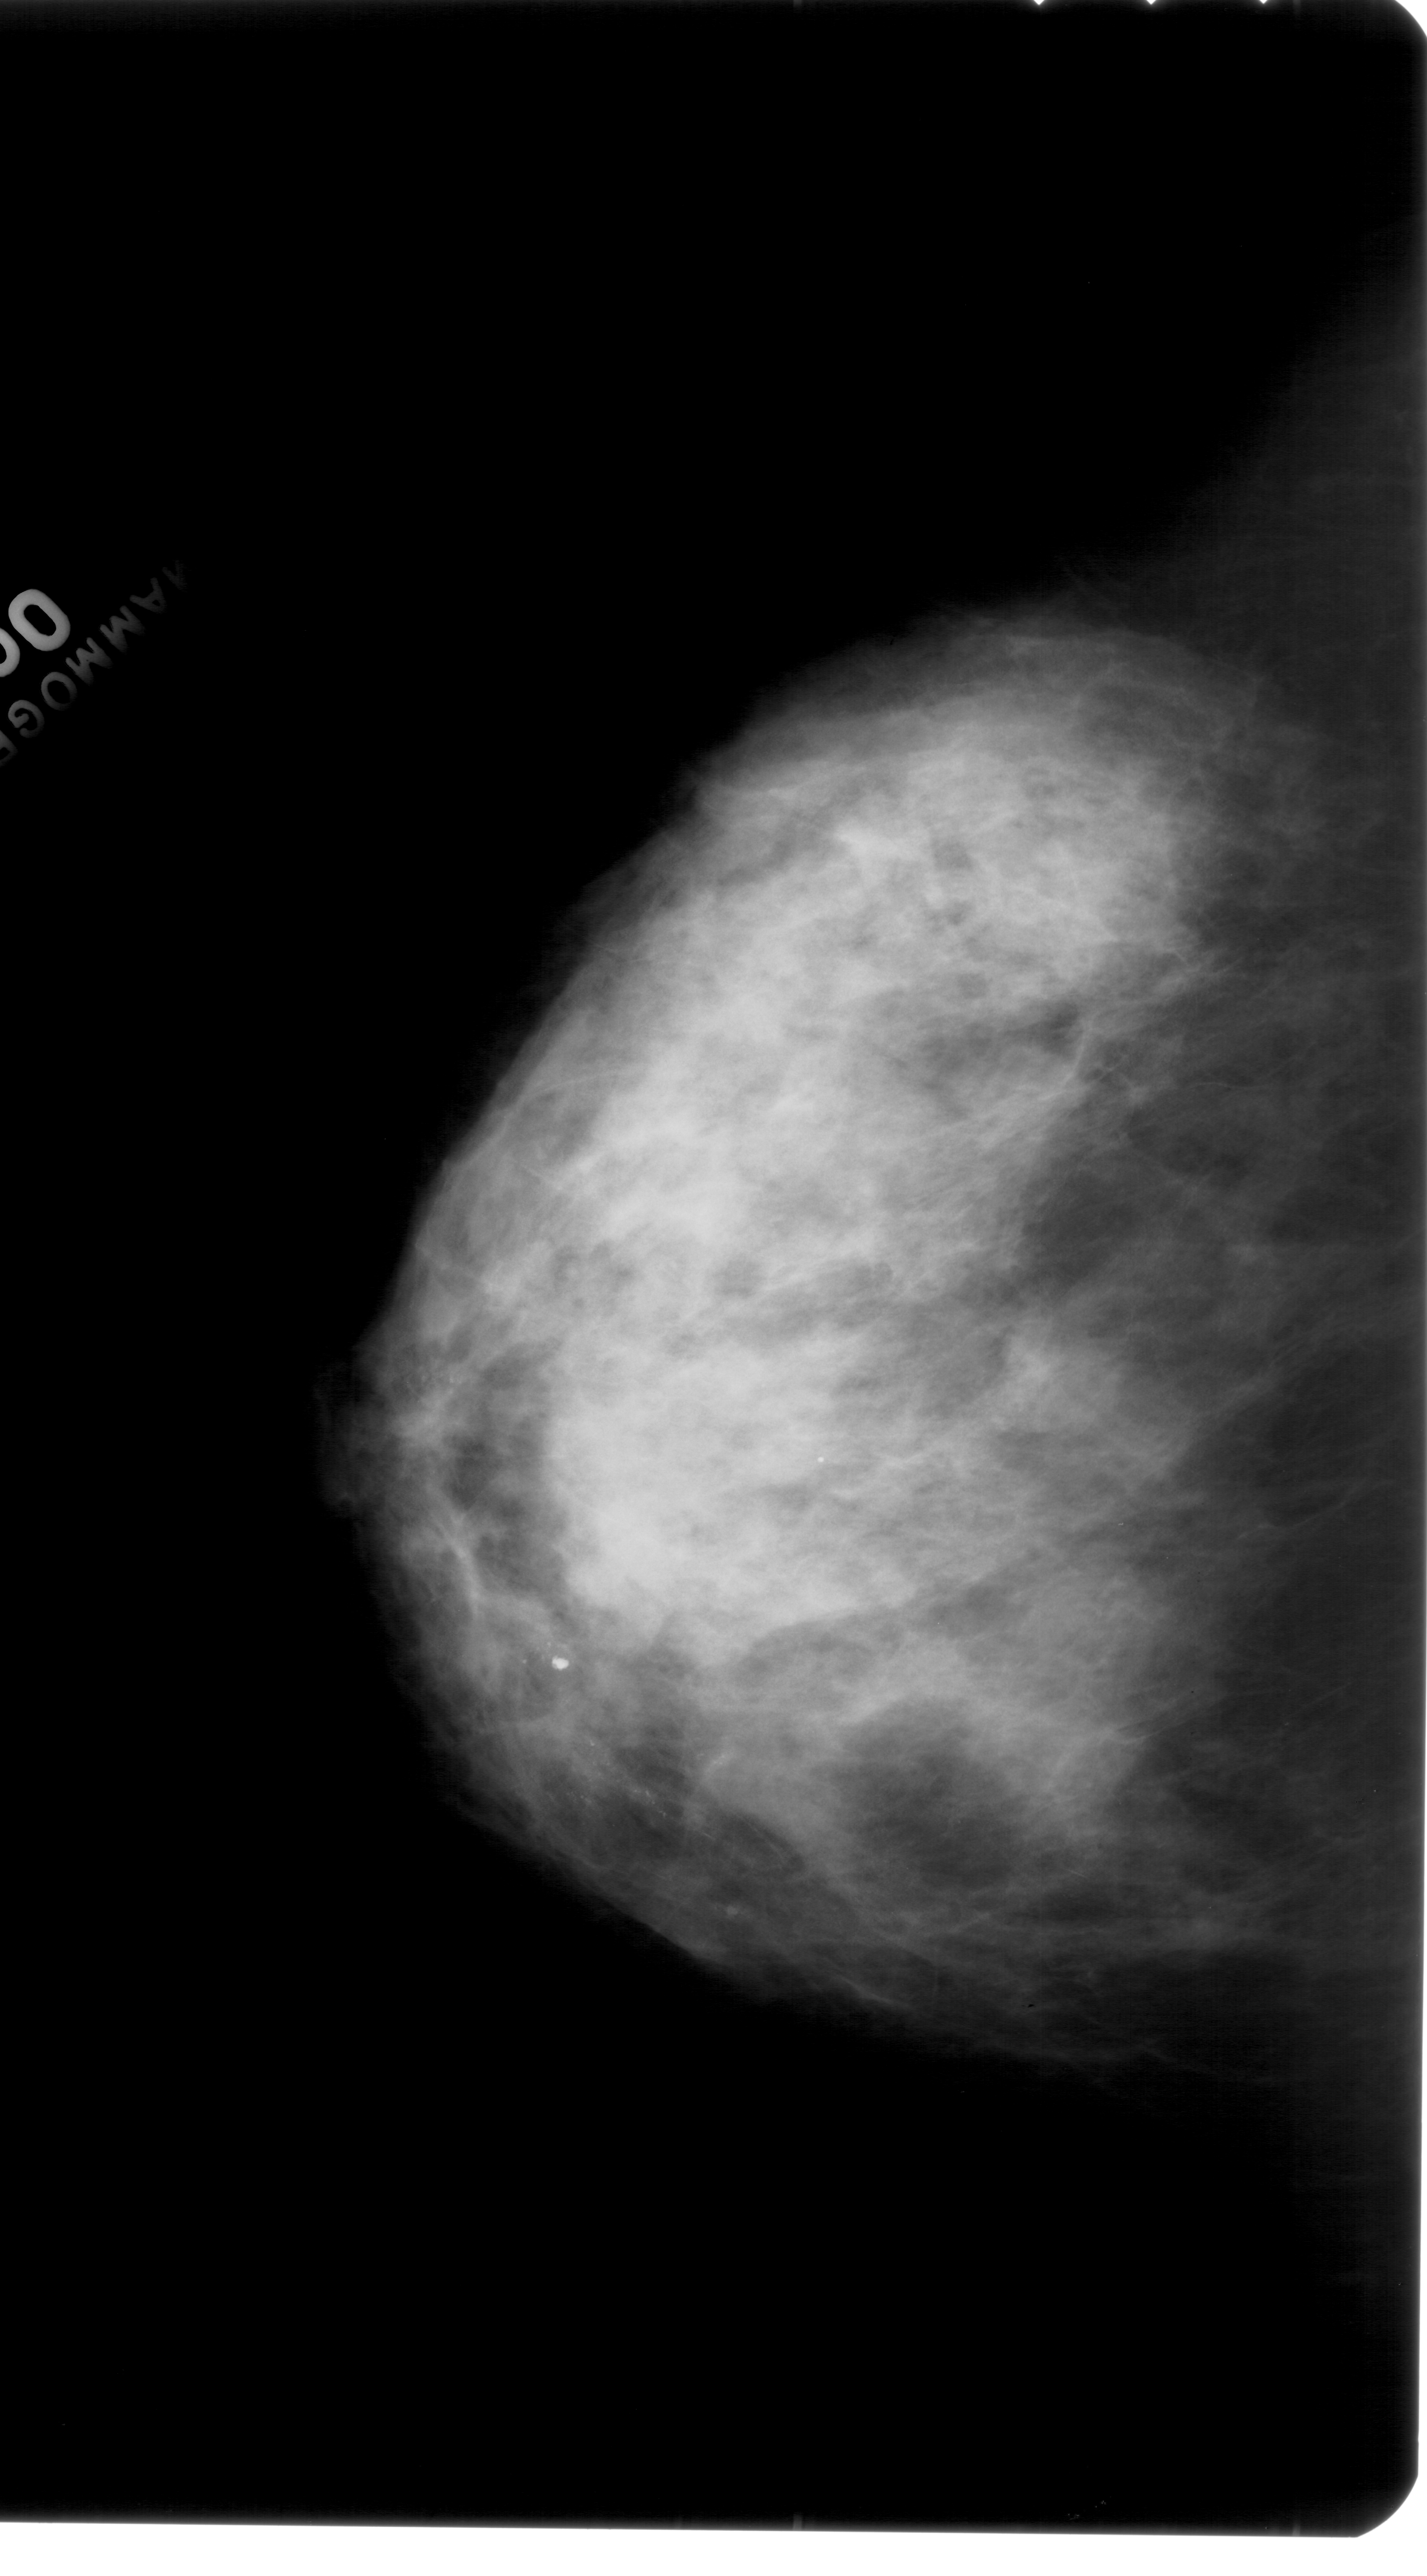
Mammogram (digitized film); left breast; craniocaudal (CC) view; BI-RADS breast density category 4 (scale 1–4).
Finding: calcifications, morphology pleomorphic, distribution linear; BI-RADS assessment category 4; subtlety rating 1 on a 1 (subtle) to 5 (obvious) scale; pathology result (as recorded, not read from the image): malignant.